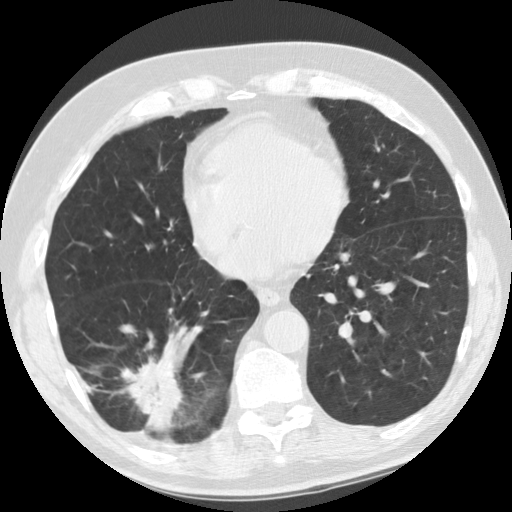
Low-dose screening chest CT, axial slice; baseline annual screen; lung window (W 1500 / L -600 HU); 2.5 mm slice thickness; standard (soft-tissue) reconstruction kernel (STANDARD). Male, age 69 years at enrolment. Former smoker at enrolment.
Expert-annotated lung lesion, bounding box <105,331,191,440> (left, top, right, bottom; pixels). The screening reader recorded 2 non-calcified nodules or masses ≥4 mm on this exam (right lower lobe, right lower lobe); which of them this box marks is not recorded. Official screen result: positive, change unspecified: nodule(s) >= 4 mm or enlarging nodule(s), mass(es), or other non-specific abnormalities suspicious for lung cancer. Participant outcome: lung cancer diagnosed 40 days after this screen — adenocarcinoma, NOS, right lower lobe, stage IIB (AJCC 6th edition), 45 mm at pathology.